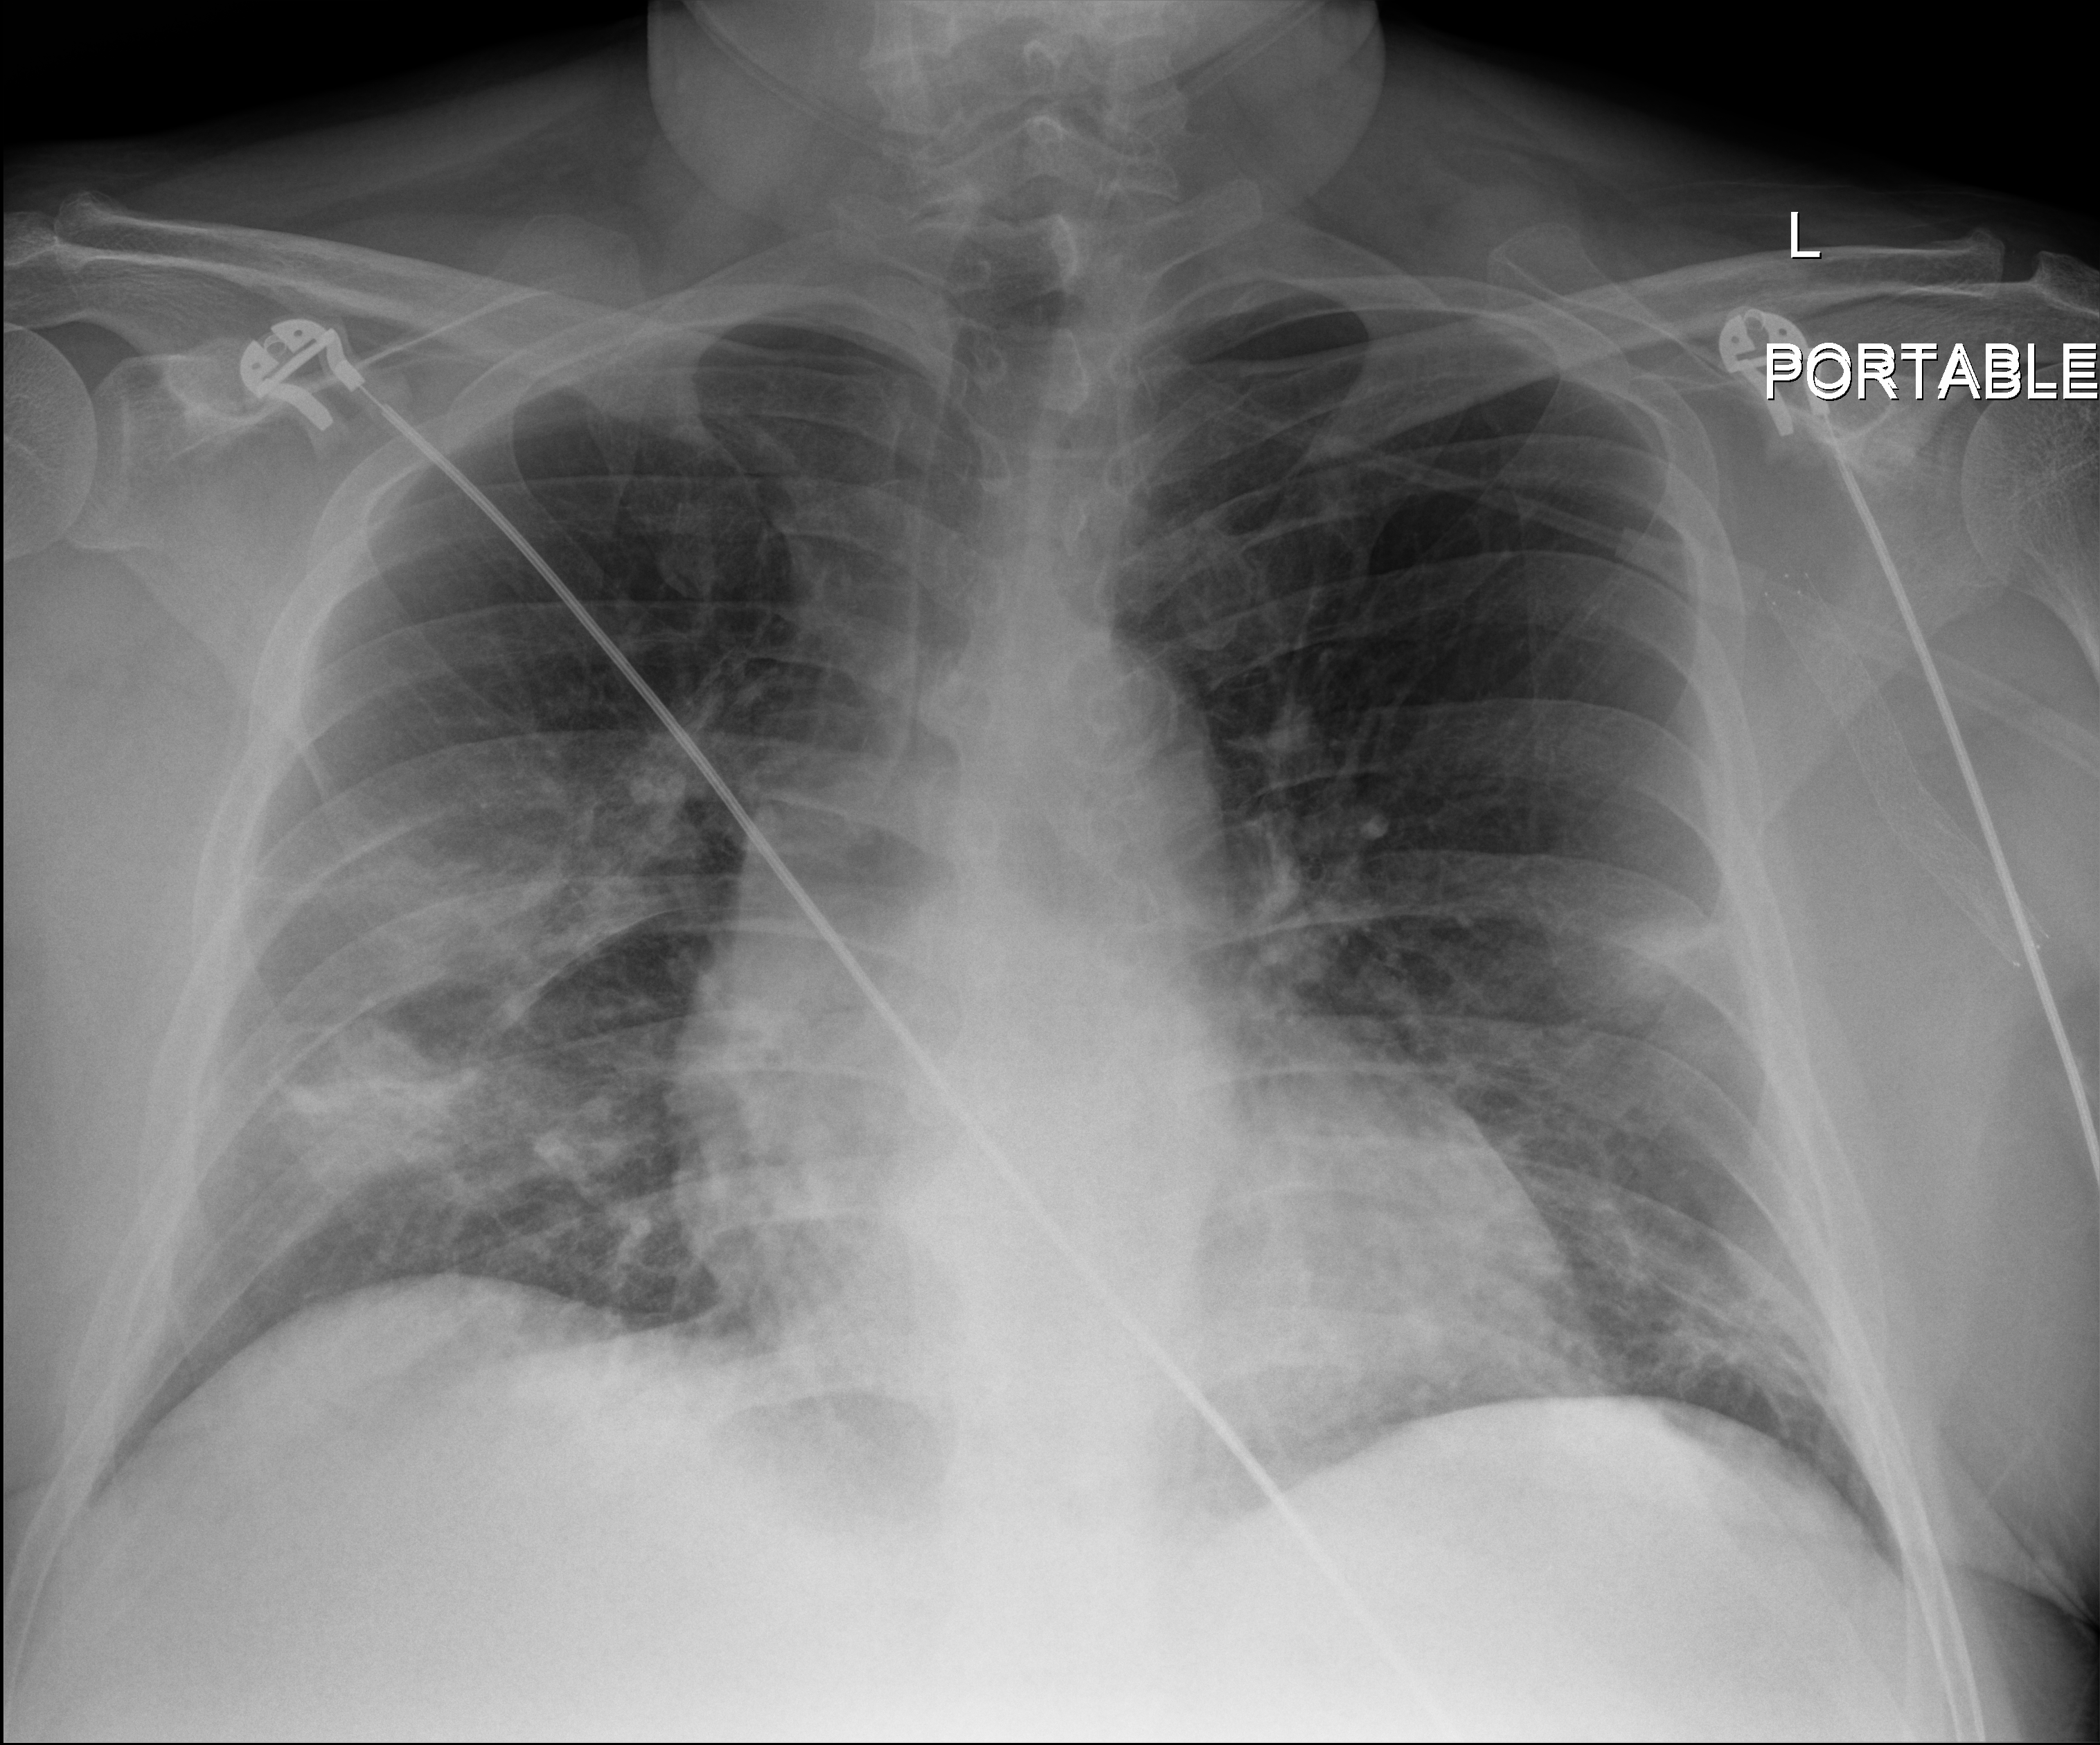
Chest radiograph; anteroposterior (AP) projection. Male patient hospitalised with COVID-19, age 18–59 years.
From the hospital-stay record, not from the radiograph (when in the stay this image was taken is not recorded):
- mechanically ventilated during this hospital stay: no